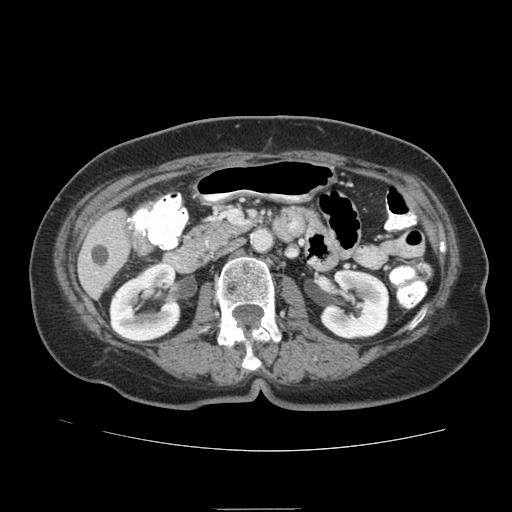
Contrast-enhanced abdominal CT (liver protocol), one axial slice; slice 27 of 95 in the series (ordered by position); soft-tissue window (W 400 / L 40 HU); 2.5 mm slice thickness; 512 × 512 image matrix, field of view 360 × 360 mm. Case-level facts recorded for this patient, not image findings: diagnosis: hepatocellular carcinoma (patient treated with transarterial chemoembolisation; whether this scan precedes or follows treatment is not stated here); TNM stage (as recorded): Stage-IVA.
Annotated regions visible in this slice (semi-automatic segmentation, software-assisted and operator-edited):
- liver parenchyma outside the tumour (the mass and vessels are separate outlines, so this box may not span the whole liver): box from (x=78, y=208) to (x=130, y=298) px